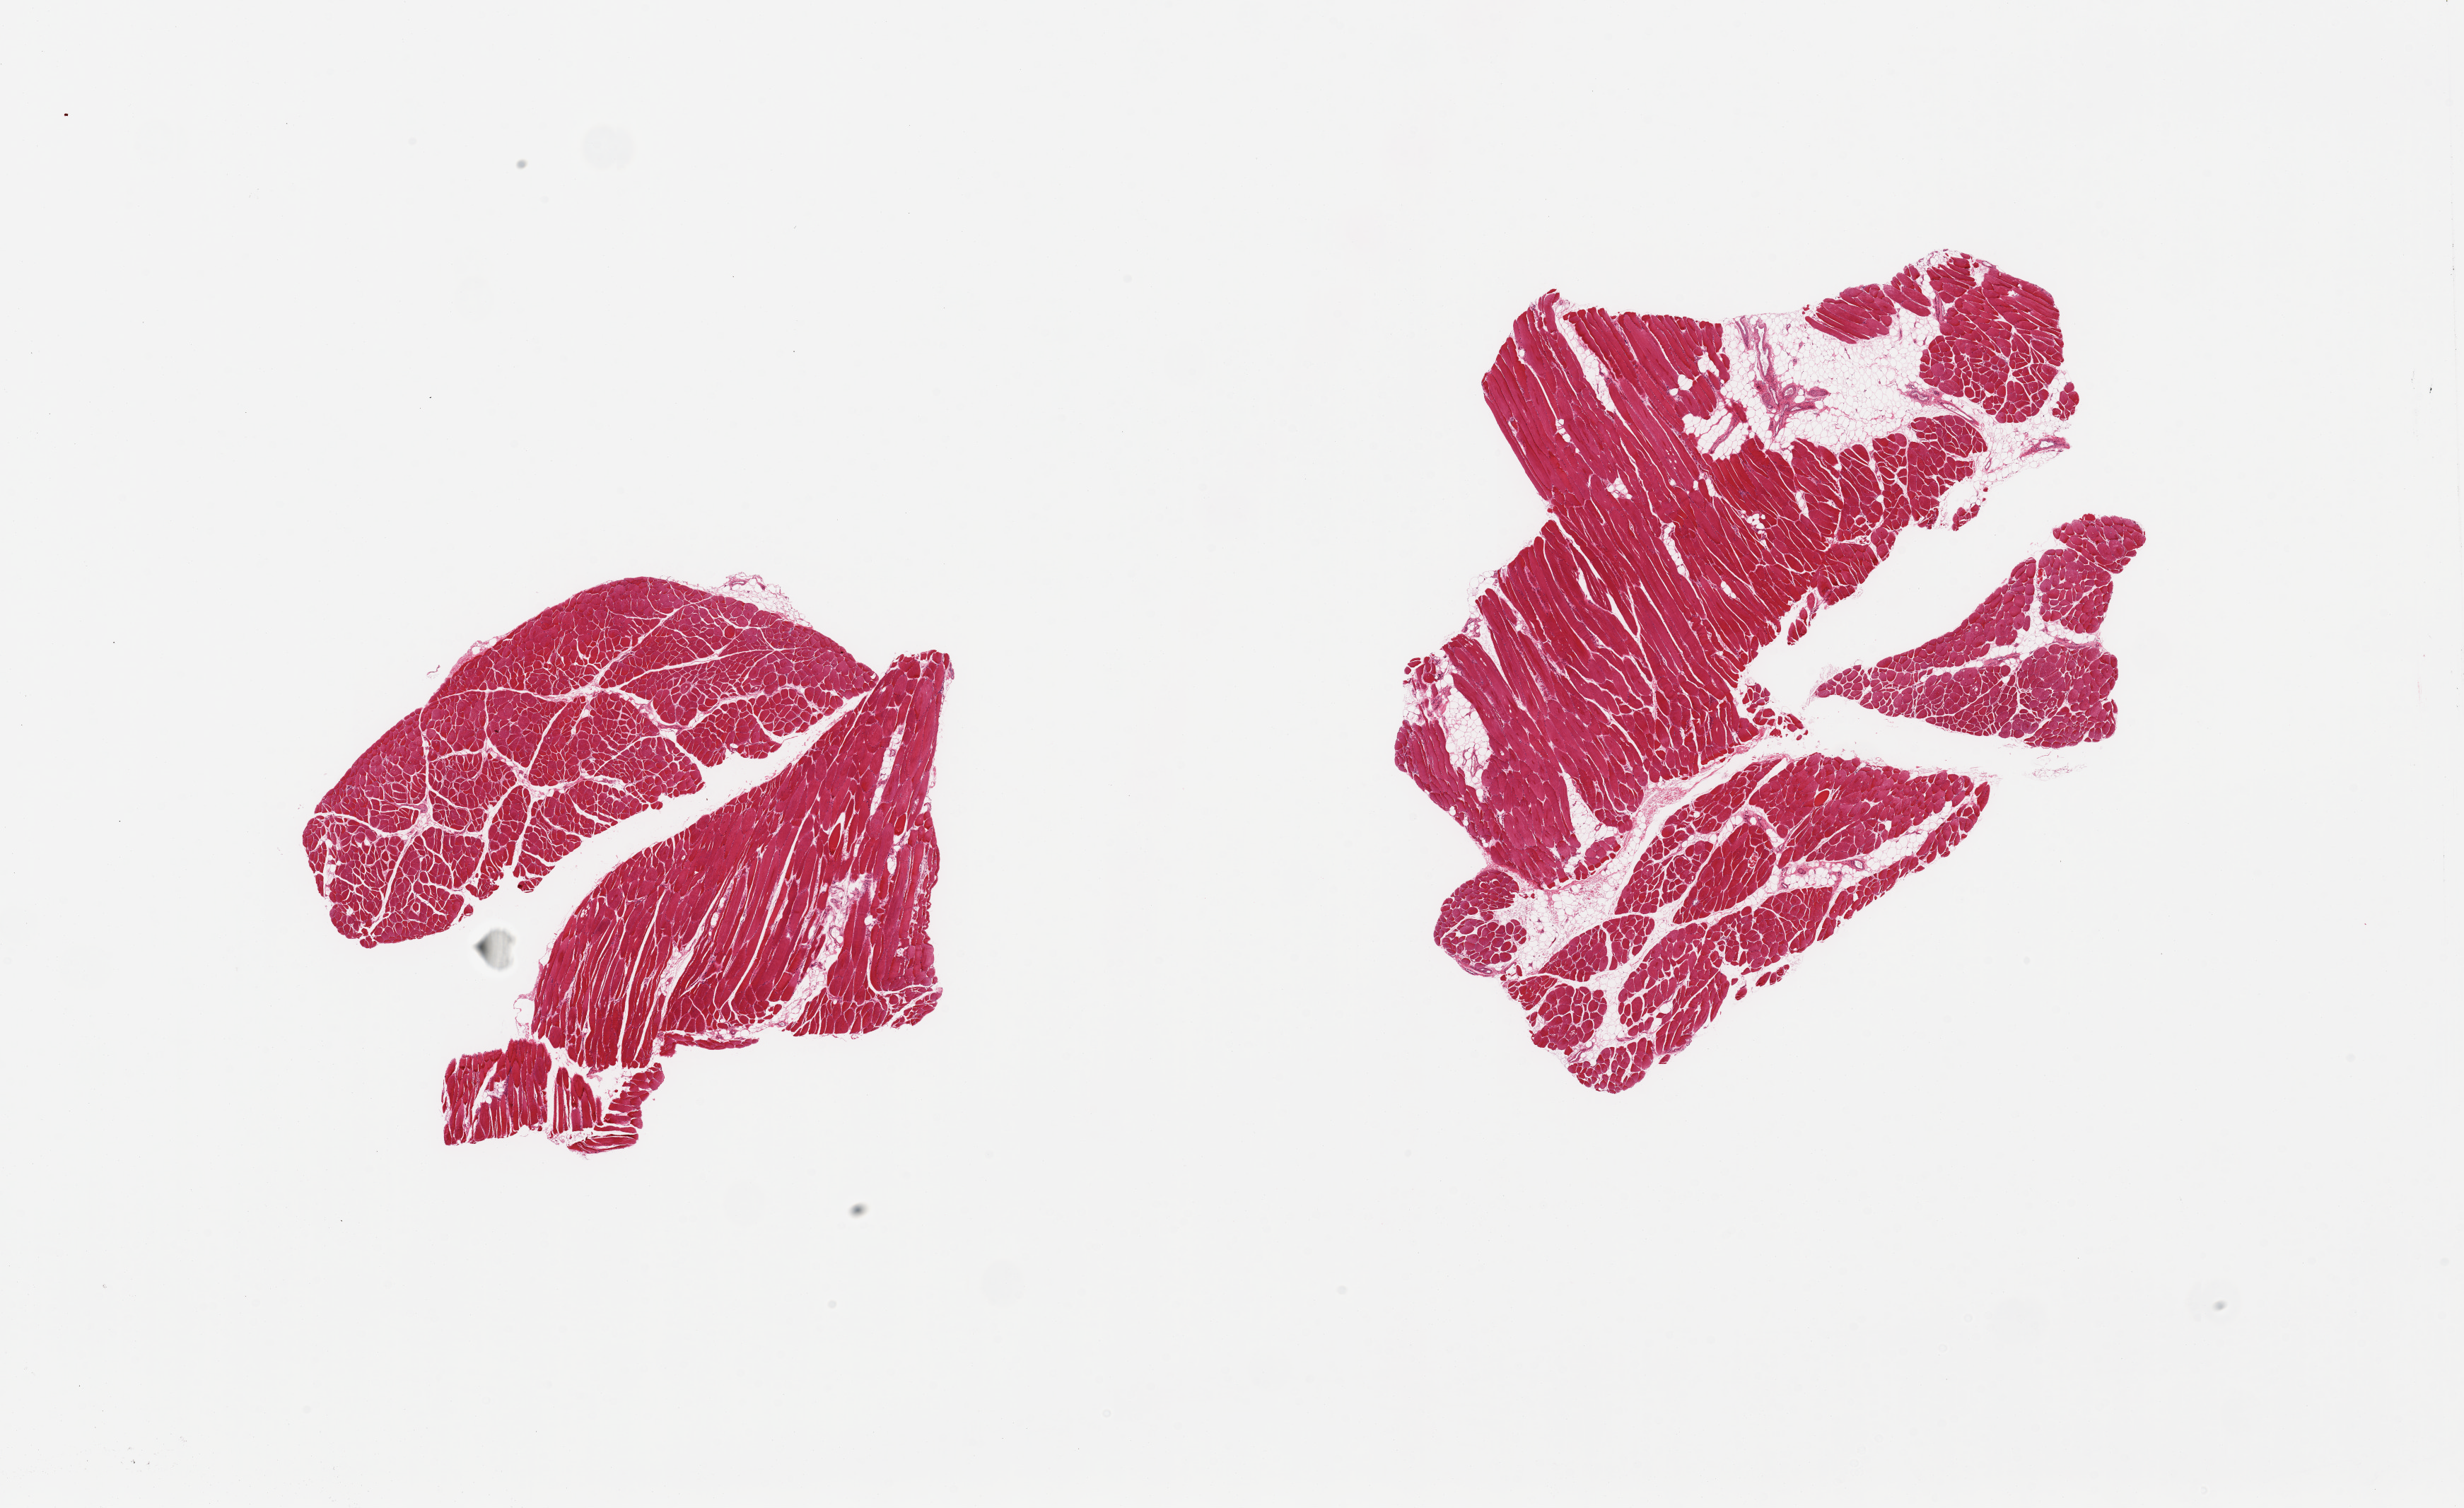
Digitized haematoxylin and eosin-stained section, whole scanned area (about 27.6 x 16.9 mm) shown as a low-resolution overview, PAXgene-fixed, paraffin-embedded tissue, target tissue: skeletal muscle, tissue donor sample. Donor sex: male.
Reviewer comment on this tissue sample: 2 pieces, interstitial fat/vascular elements are 10-20% of tissue.